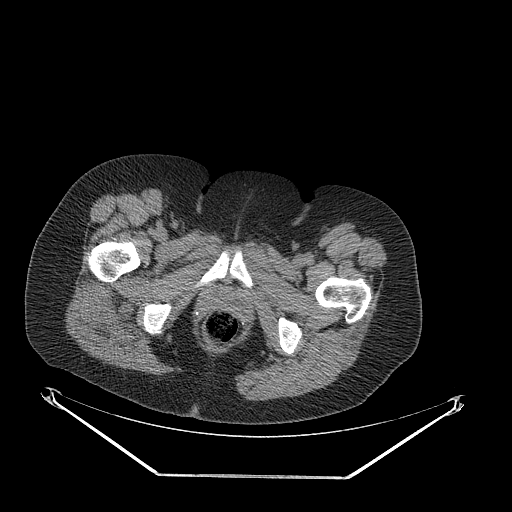
CT of an extremity soft-tissue mass (from a PET/CT study), one axial slice. Slice 60 of 257 in the series (ordered by position). Reconstruction kernel STANDARD. Soft-tissue window (W 400 / L 40 HU). 3.75 mm slice thickness. 512 × 512 image matrix, field of view 500 × 500 mm. Female patient. From the clinical record (not read from this slice): histological type: synovial sarcoma; grade: intermediate; site of the primary tumour: right buttock.
Structures marked on this image (expert contour drawn on MRI and transferred to this co-registered scan by the dataset authors):
- gross tumour volume including surrounding oedema: box from (x=87, y=288) to (x=156, y=344) px
- gross tumour volume (mass): (x=98, y=288)–(x=127, y=309)